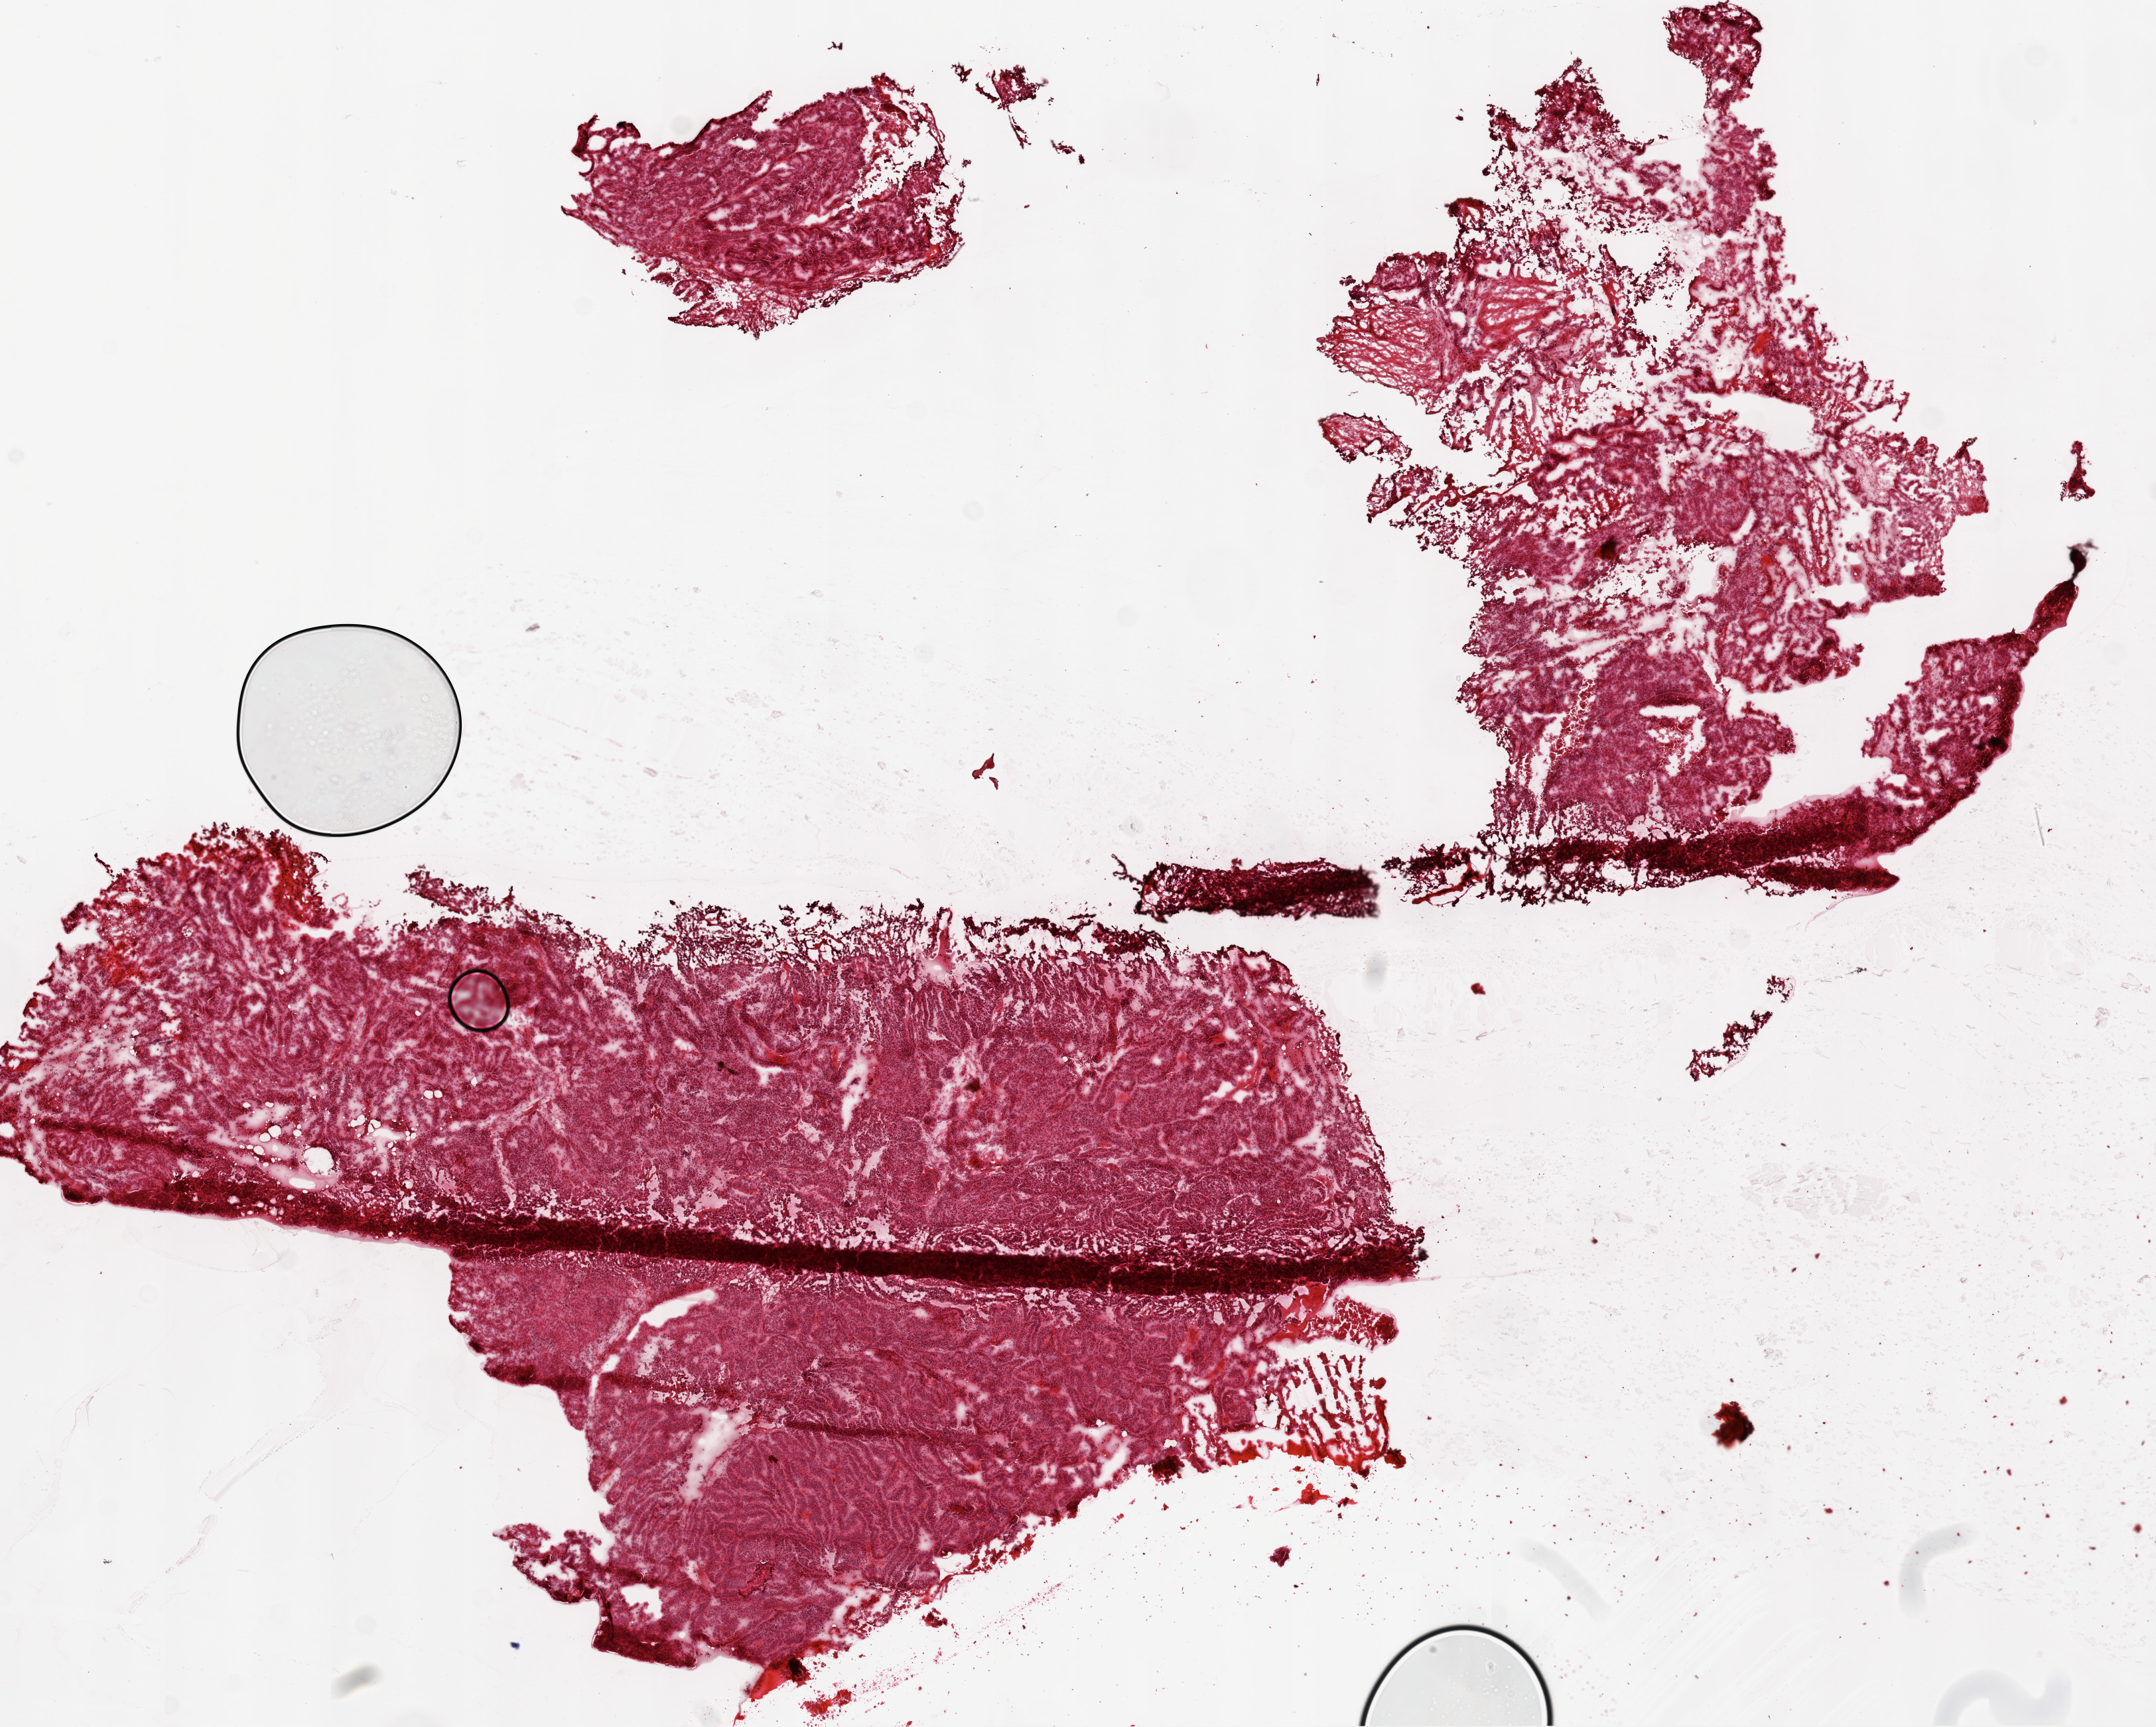
Whole-slide histology image, H&E-stained — whole scanned area (about 13.0 x 10.4 mm) shown as a low-resolution overview; frozen section from the top of the tissue portion; ovary, primary tumour sample. Female patient; age at initial diagnosis 71 years. Histologic grade: G3 (poorly differentiated). Composition of this section per pathologist review: tumour cells 95%, tumour nuclei 95%, normal cells 0%, stromal cells 4%, necrosis 1%.
• FIGO stage: IIIC
• pathologic diagnosis: Serous cystadenocarcinoma, NOS